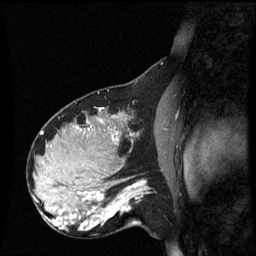
Breast MRI (dynamic contrast-enhanced), one sagittal slice; position 35 of 60 along the scan axis; dynamic contrast-enhanced series, image 2 of 3 at this slice position (ordered by acquisition); 1.5 T; TE 4.2 ms, TR 8.9 ms; 2.2 mm slice thickness; 256 × 256 image matrix, field of view 220 × 220 mm. Patient: female, 31 years. Case-level facts recorded for this patient, not image findings: setting: breast cancer imaged before/during neoadjuvant chemotherapy; receptor status: HR-positive, HER2-negative.
Outlined on this slice (semi-automatically segmented with operator editing):
- analysis volume of interest (the breast-tissue region the enhancement analysis was run in; not a lesion): bounding box (x1, y1, x2, y2) in pixels: (90, 180, 151, 231)
- tumour enhancement mask (voxels above the 70 % enhancement threshold inside the analysis volume of interest): (90, 184, 144, 229)